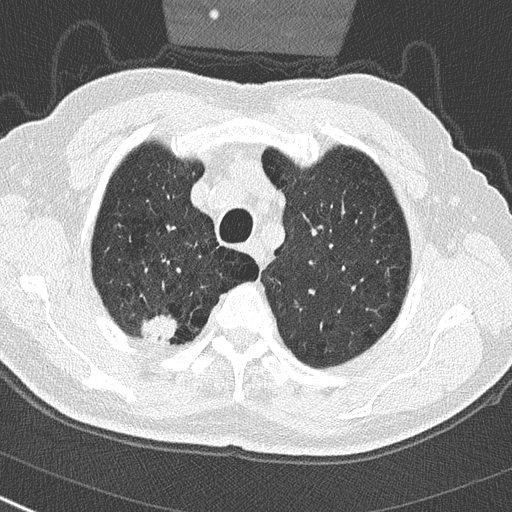
Low-dose screening chest CT, axial slice; first (baseline) screen; lung window (W 1500 / L -600 HU); slice 52 of 290 in the series; 512 × 512 image matrix, field of view 300 × 300 mm. Male, age 65 years at enrolment. Current smoker at enrolment.
Expert-annotated lung lesion, box from (x=135, y=304) to (x=184, y=351) px. Reader record for this screening exam (exam-level; its link to the box is not recorded): non-calcified nodule or mass ≥4 mm, right upper lobe, 24 × 19 mm, spiculated (stellate) margins, soft tissue attenuation. Lung cancer was diagnosed 32 days after this screen: non-small cell carcinoma, right upper lobe, poorly differentiated (G3), stage IA (AJCC 6th edition), 29 mm at pathology.